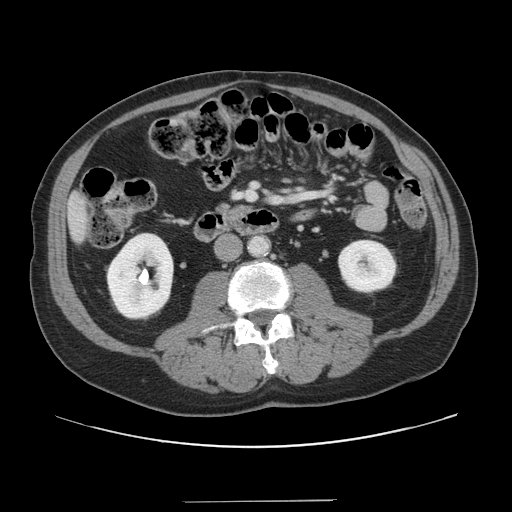
Contrast-enhanced abdominal CT, one axial slice; position 37 of 151 along the scan axis; intravenous contrast given; soft-tissue window (W 400 / L 40 HU); 2.5 mm slice thickness; 512 × 512 image matrix, field of view 399 × 399 mm. Male patient, age 63 years. From the clinical record (not read from this slice): diagnosis: colorectal cancer liver metastases, imaged before liver resection; multiple liver metastases: no; largest metastasis: 2.1 cm.
Annotated regions visible in this slice (expert manual segmentation):
- liver: bounding box <69,195,88,240> (left, top, right, bottom; pixels)
- planned liver remnant (the part of the liver to remain after resection): <69,194,89,241>
- portal vein (with intrahepatic branches): <236,192,255,200>